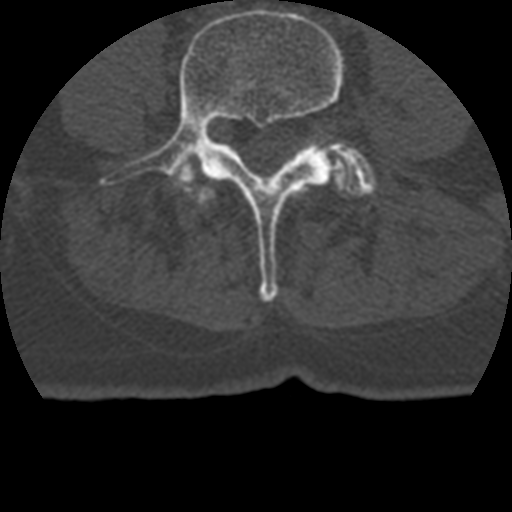
CT including the spine, one axial slice; position 64 of 399 along the scan axis; 120 kVp; bone window (W 1800 / L 400 HU); 512 × 512 image matrix. Patient age 69 years. From the clinical record (not read from this slice): primary cancer: prostate.
Outlined on this slice (semi-automatically segmented with operator editing):
- L3 vertebra: bounding box [x1, y1, x2, y2] px = [200, 186, 215, 206]
- L4 vertebra: [102, 9, 344, 302]
- L5 vertebra: [330, 143, 376, 195]